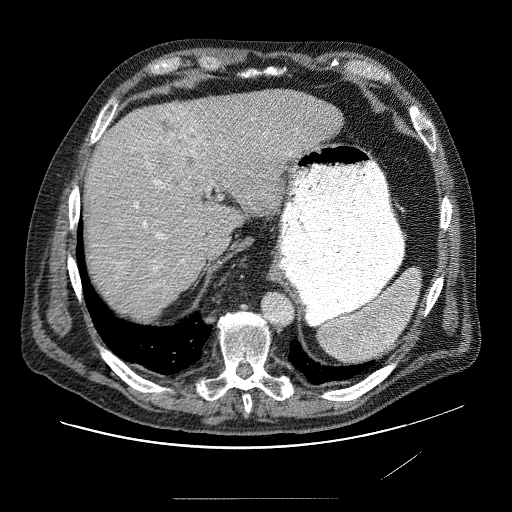
Contrast-enhanced abdominal CT (liver protocol), one axial slice. Slice 60 of 89 in the series (ordered by position). Reconstruction kernel STANDARD. Soft-tissue window (W 400 / L 40 HU). 2.5 mm slice thickness. 512 × 512 image matrix. Case-level facts recorded for this patient, not image findings: diagnosis: hepatocellular carcinoma (patient treated with transarterial chemoembolisation; whether this scan precedes or follows treatment is not stated here); TNM stage (as recorded): Stage-IVA; Child-Pugh class: A; tumour differentiation: moderately differentiated; tumour nodularity: multinodular.
Structures marked on this image (semi-automatically segmented with operator editing):
- liver parenchyma outside the tumour (the mass and vessels are separate outlines, so this box may not span the whole liver): bounding box (x1, y1, x2, y2) in pixels: (84, 90, 346, 304)
- mass: (103, 100, 281, 283)
- liver vessels: (120, 130, 324, 275)